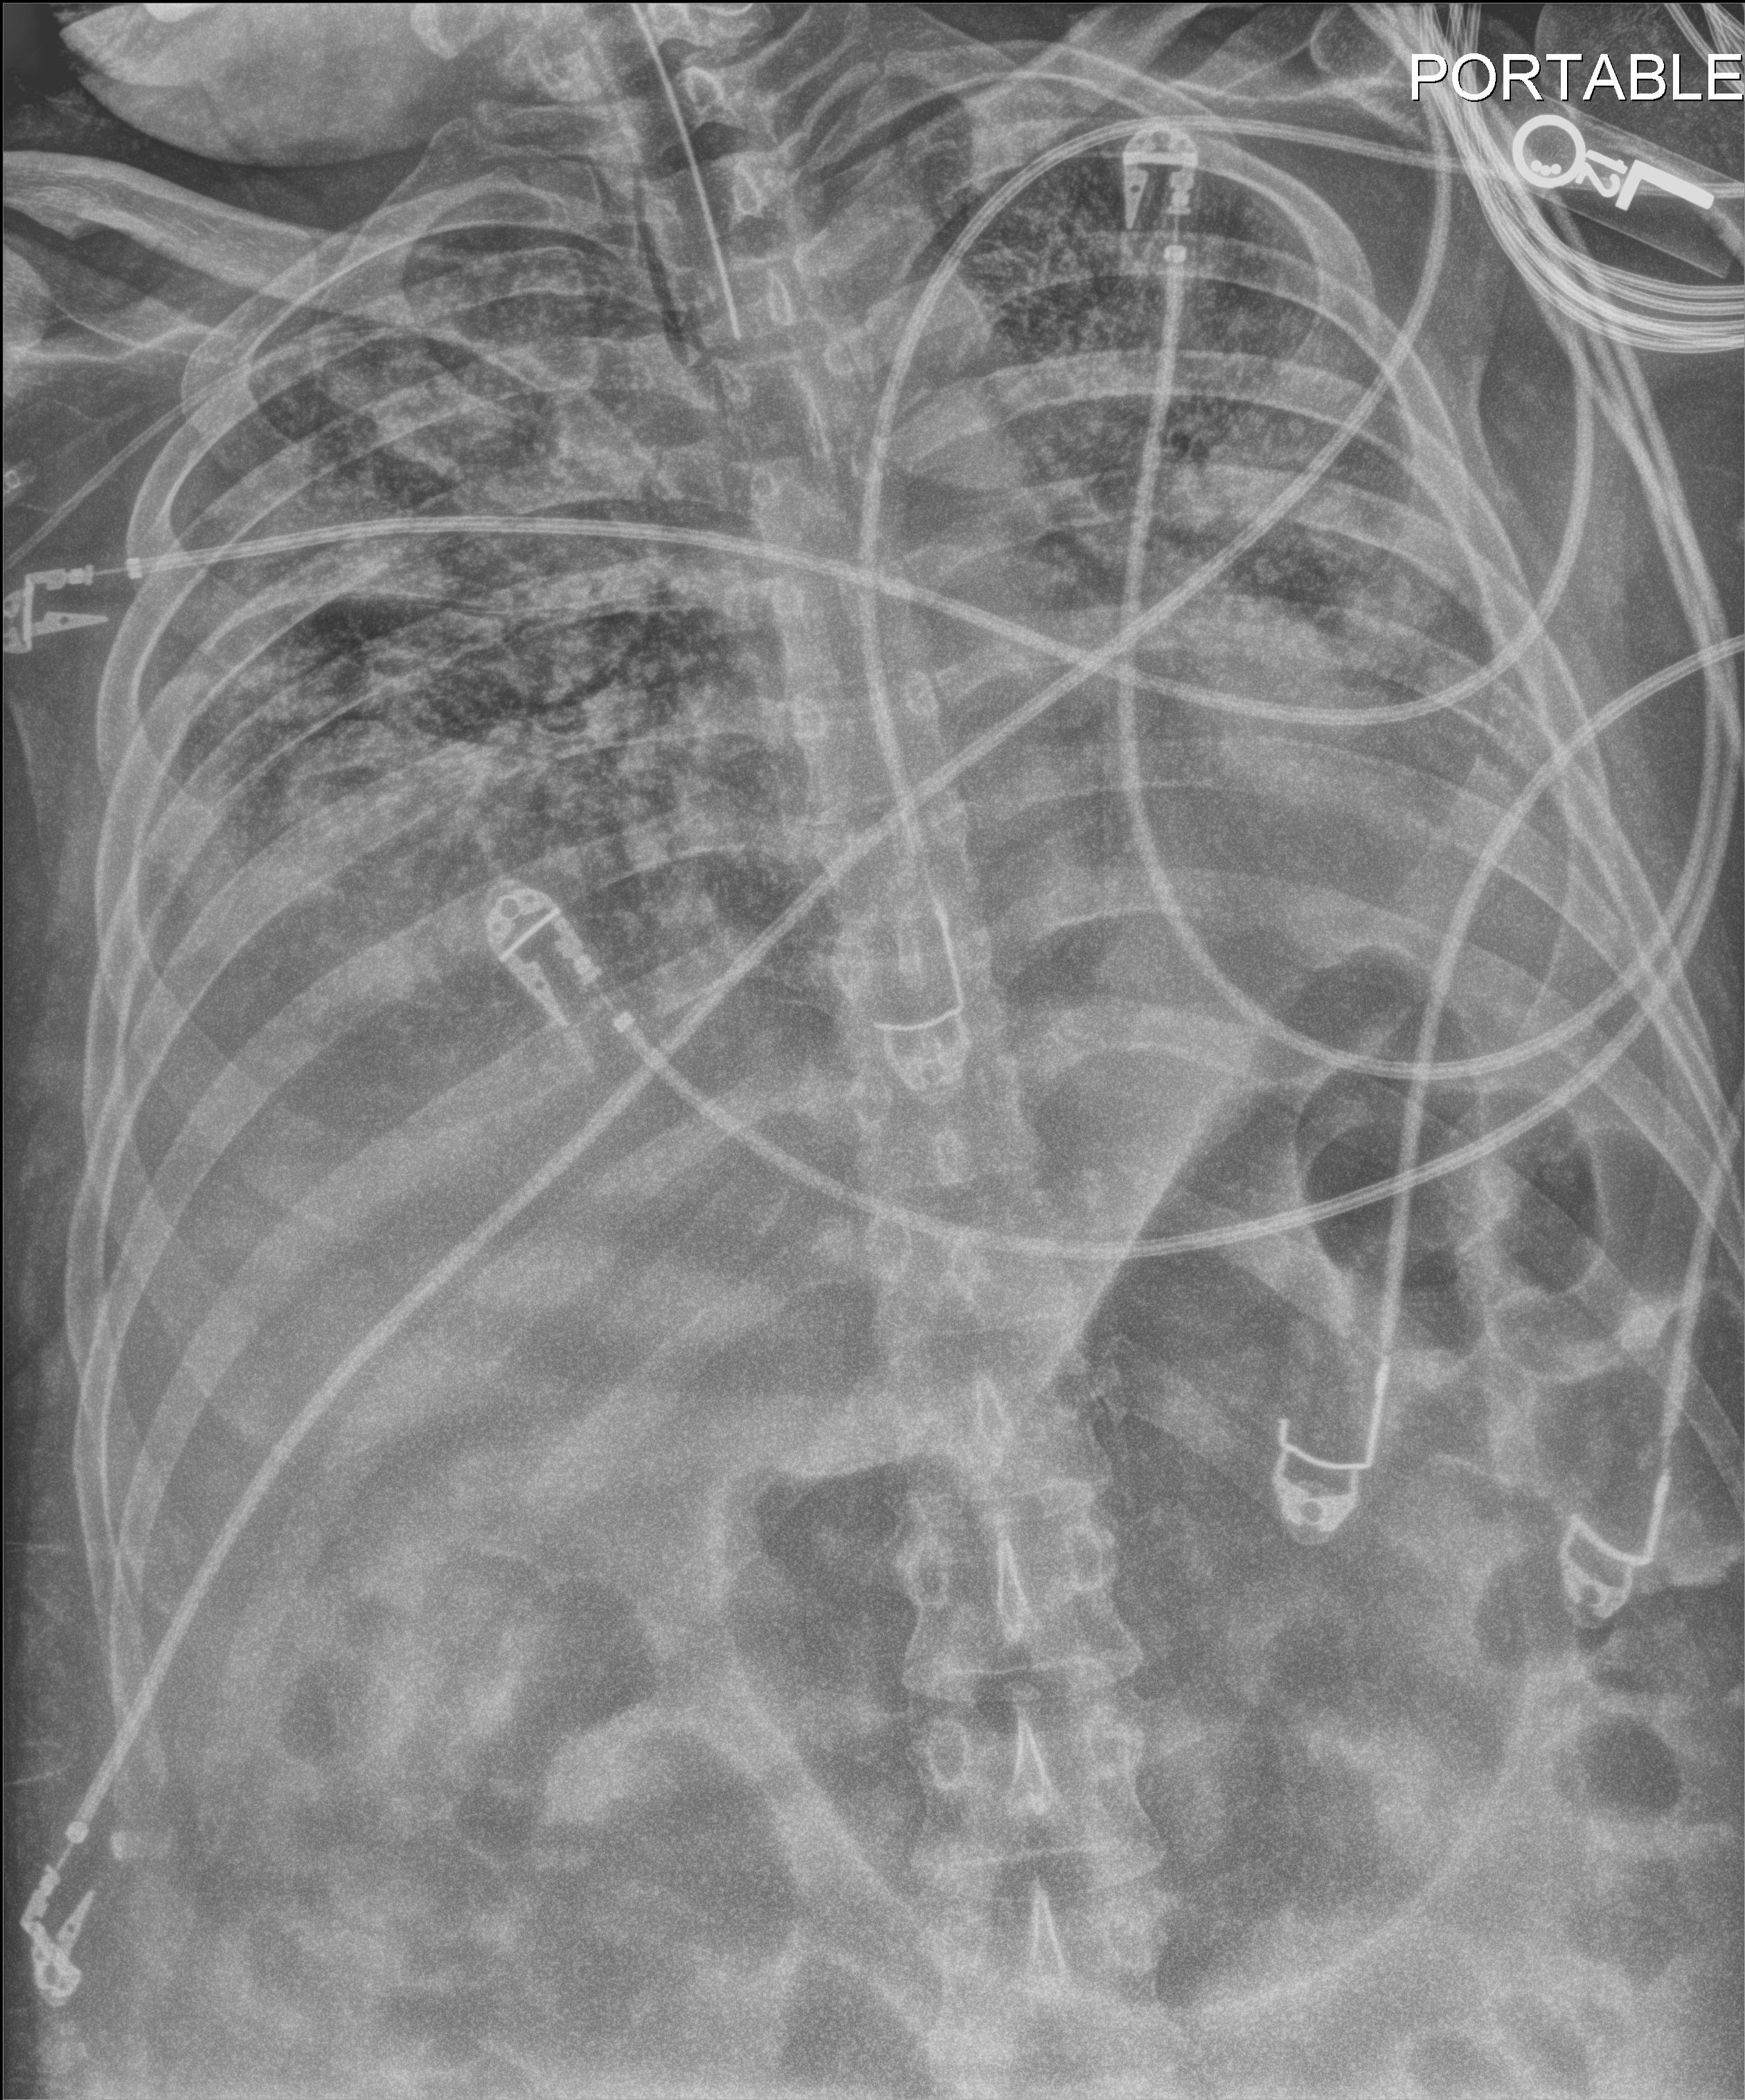
Chest X-ray (portable); anteroposterior (AP) projection. Patient hospitalised with COVID-19; male, aged 18–59 years.
Hospital-stay facts (about this admission, not read from this image; timing relative to this image not recorded): admitted to intensive care during this hospital stay: yes; mechanically ventilated during this hospital stay: yes.